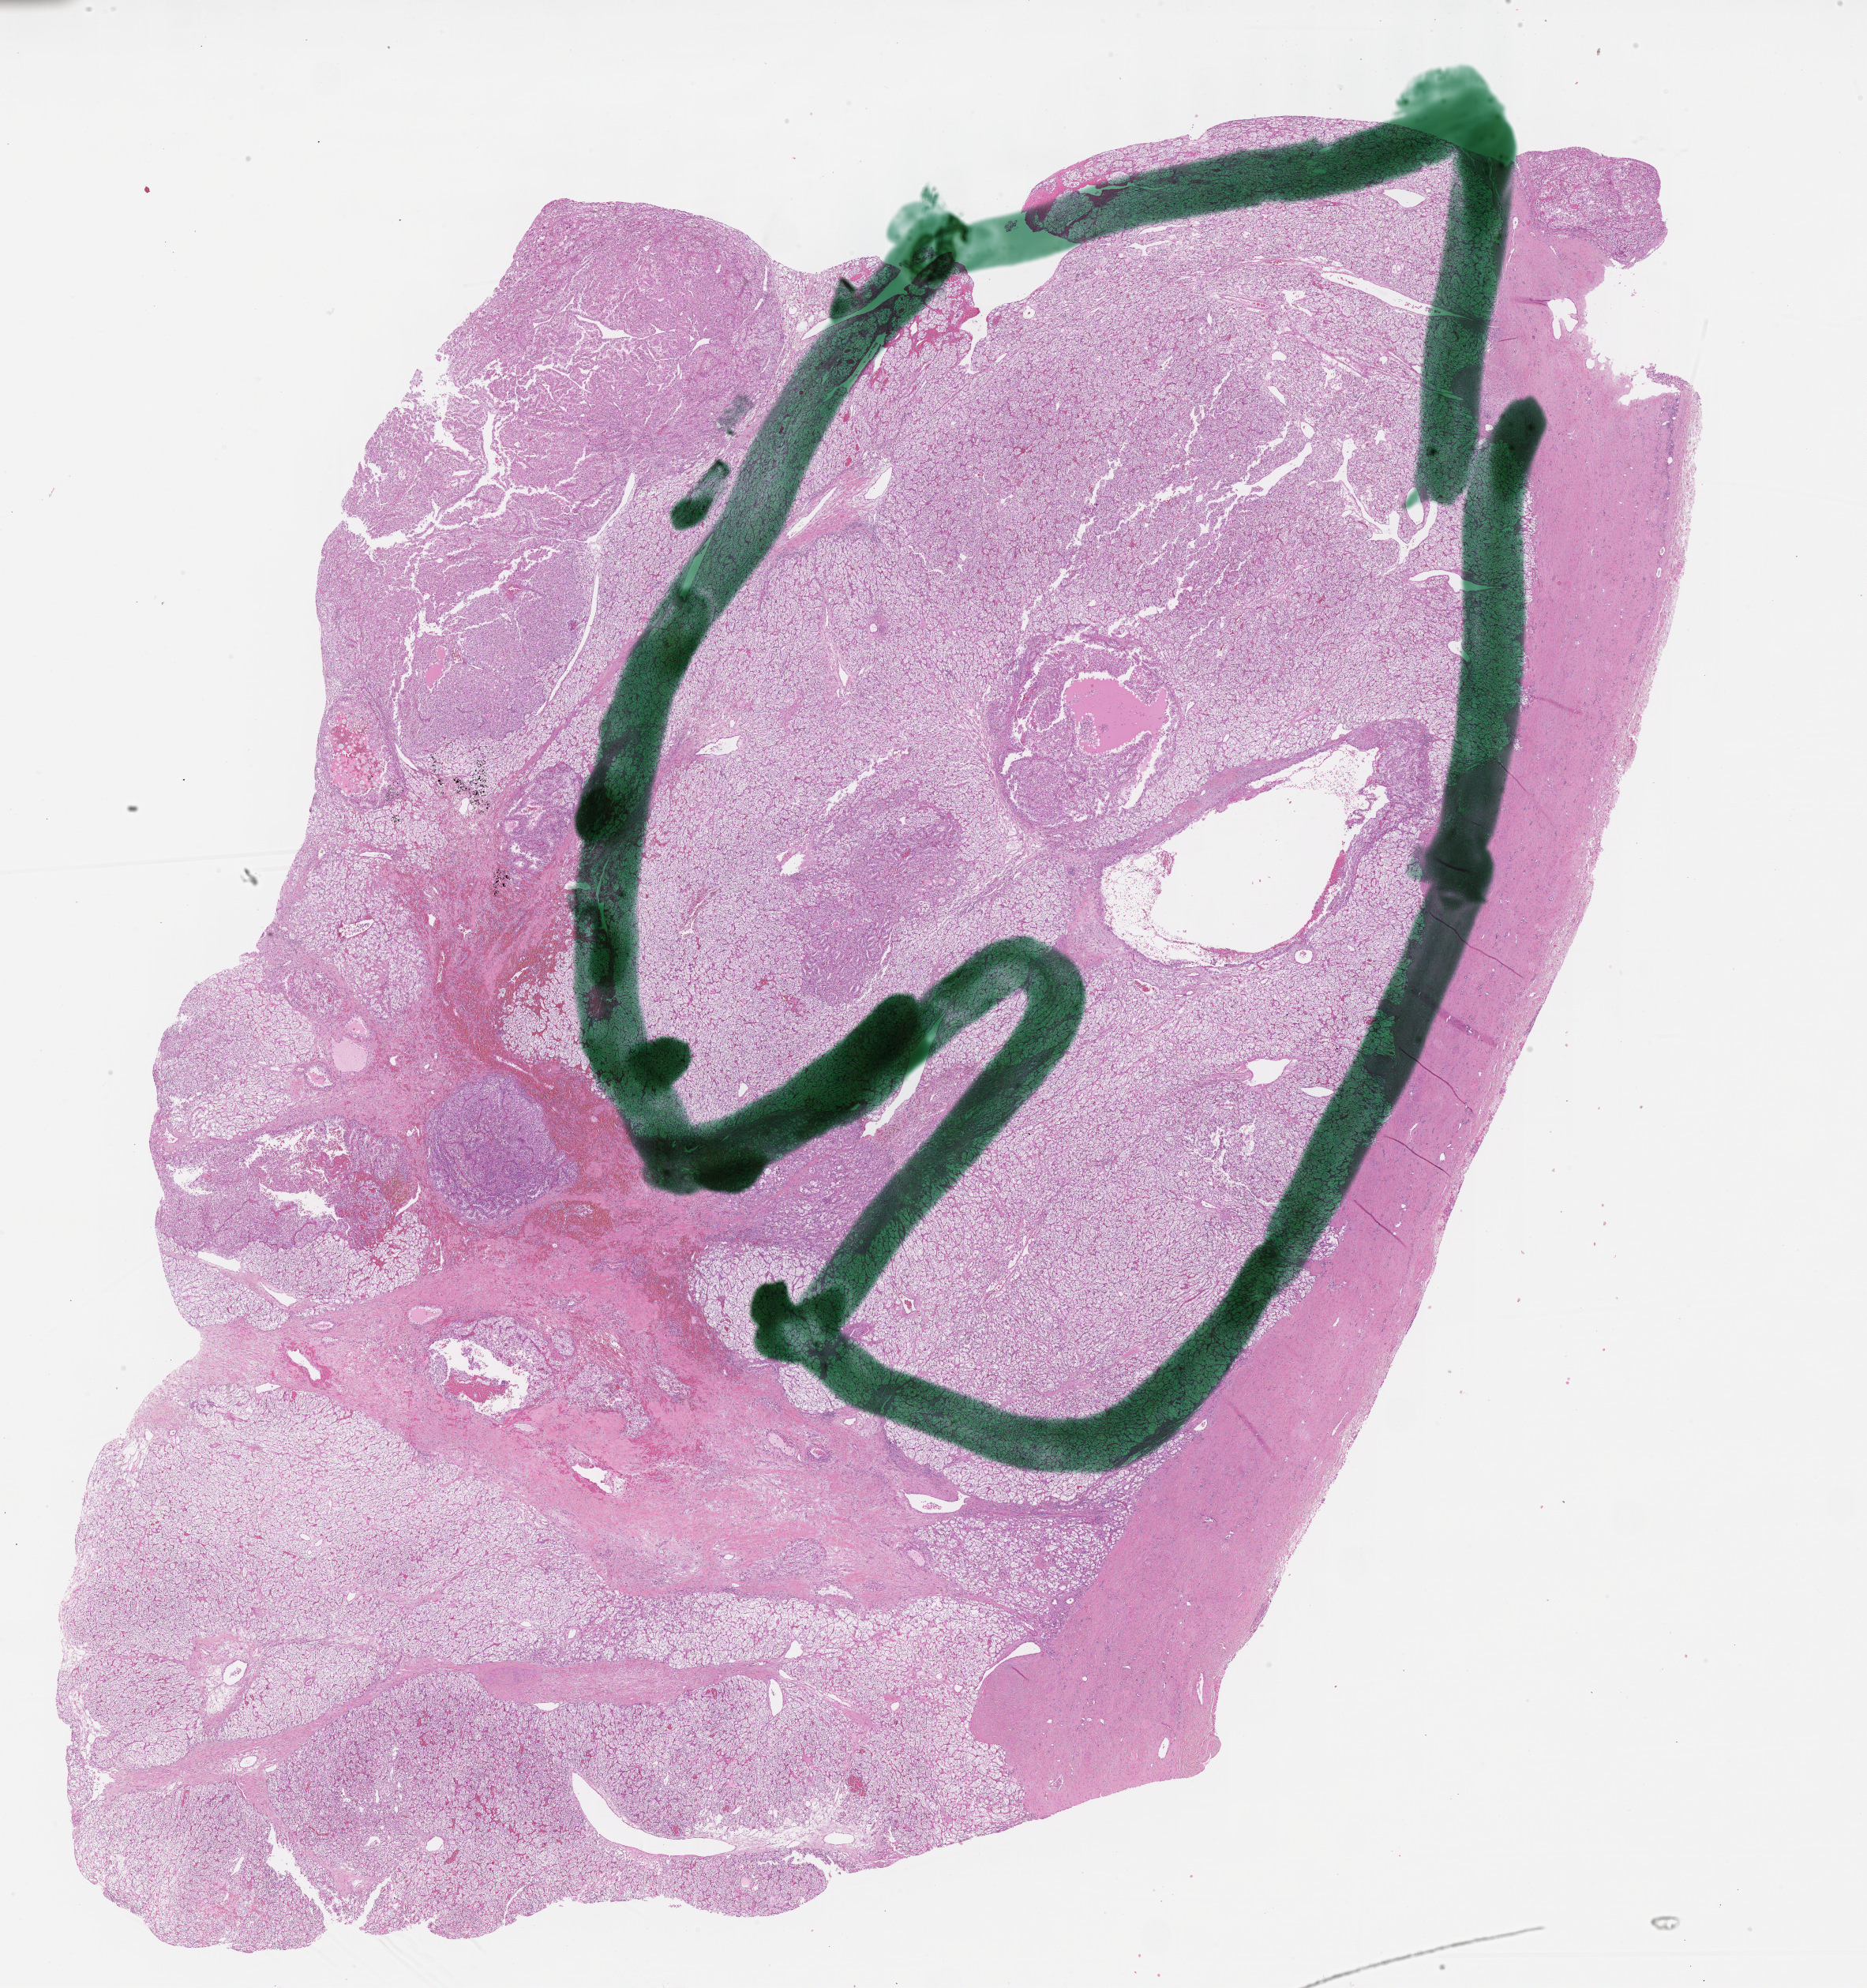
Digitized Hematoxylin and eosin (H&E) stained tissue section (whole slide), shown as a low-resolution overview of the whole scanned area (about 19.1 x 20.4 mm, from a 40x scan), formalin-fixed paraffin-embedded (FFPE) diagnostic section, sample: primary tumour, kidney. Female patient; age at initial diagnosis 46 years.
Diagnosis: Clear cell adenocarcinoma, NOS.